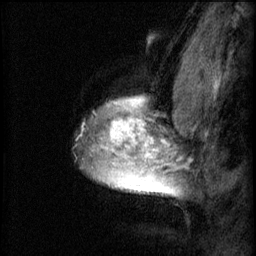
Breast MRI (dynamic contrast-enhanced), one sagittal slice; slice 50 of 60 in the series (ordered by position); 3 images stored at this slice position (order not interpretable as contrast timing); 1.5 T; TE 4.2 ms, TR 8.2 ms; 2 mm slice thickness; 256 × 256 image matrix, field of view 180 × 180 mm. Patient: female, 40 years.
Annotated regions visible in this slice (semi-automatically segmented with operator editing):
- analysis volume of interest (the breast-tissue region the enhancement analysis was run in; not a lesion): box from (x=78, y=84) to (x=167, y=195) px
- tumour enhancement mask (voxels above the 70 % enhancement threshold inside the analysis volume of interest): (x=93, y=98)–(x=167, y=195)